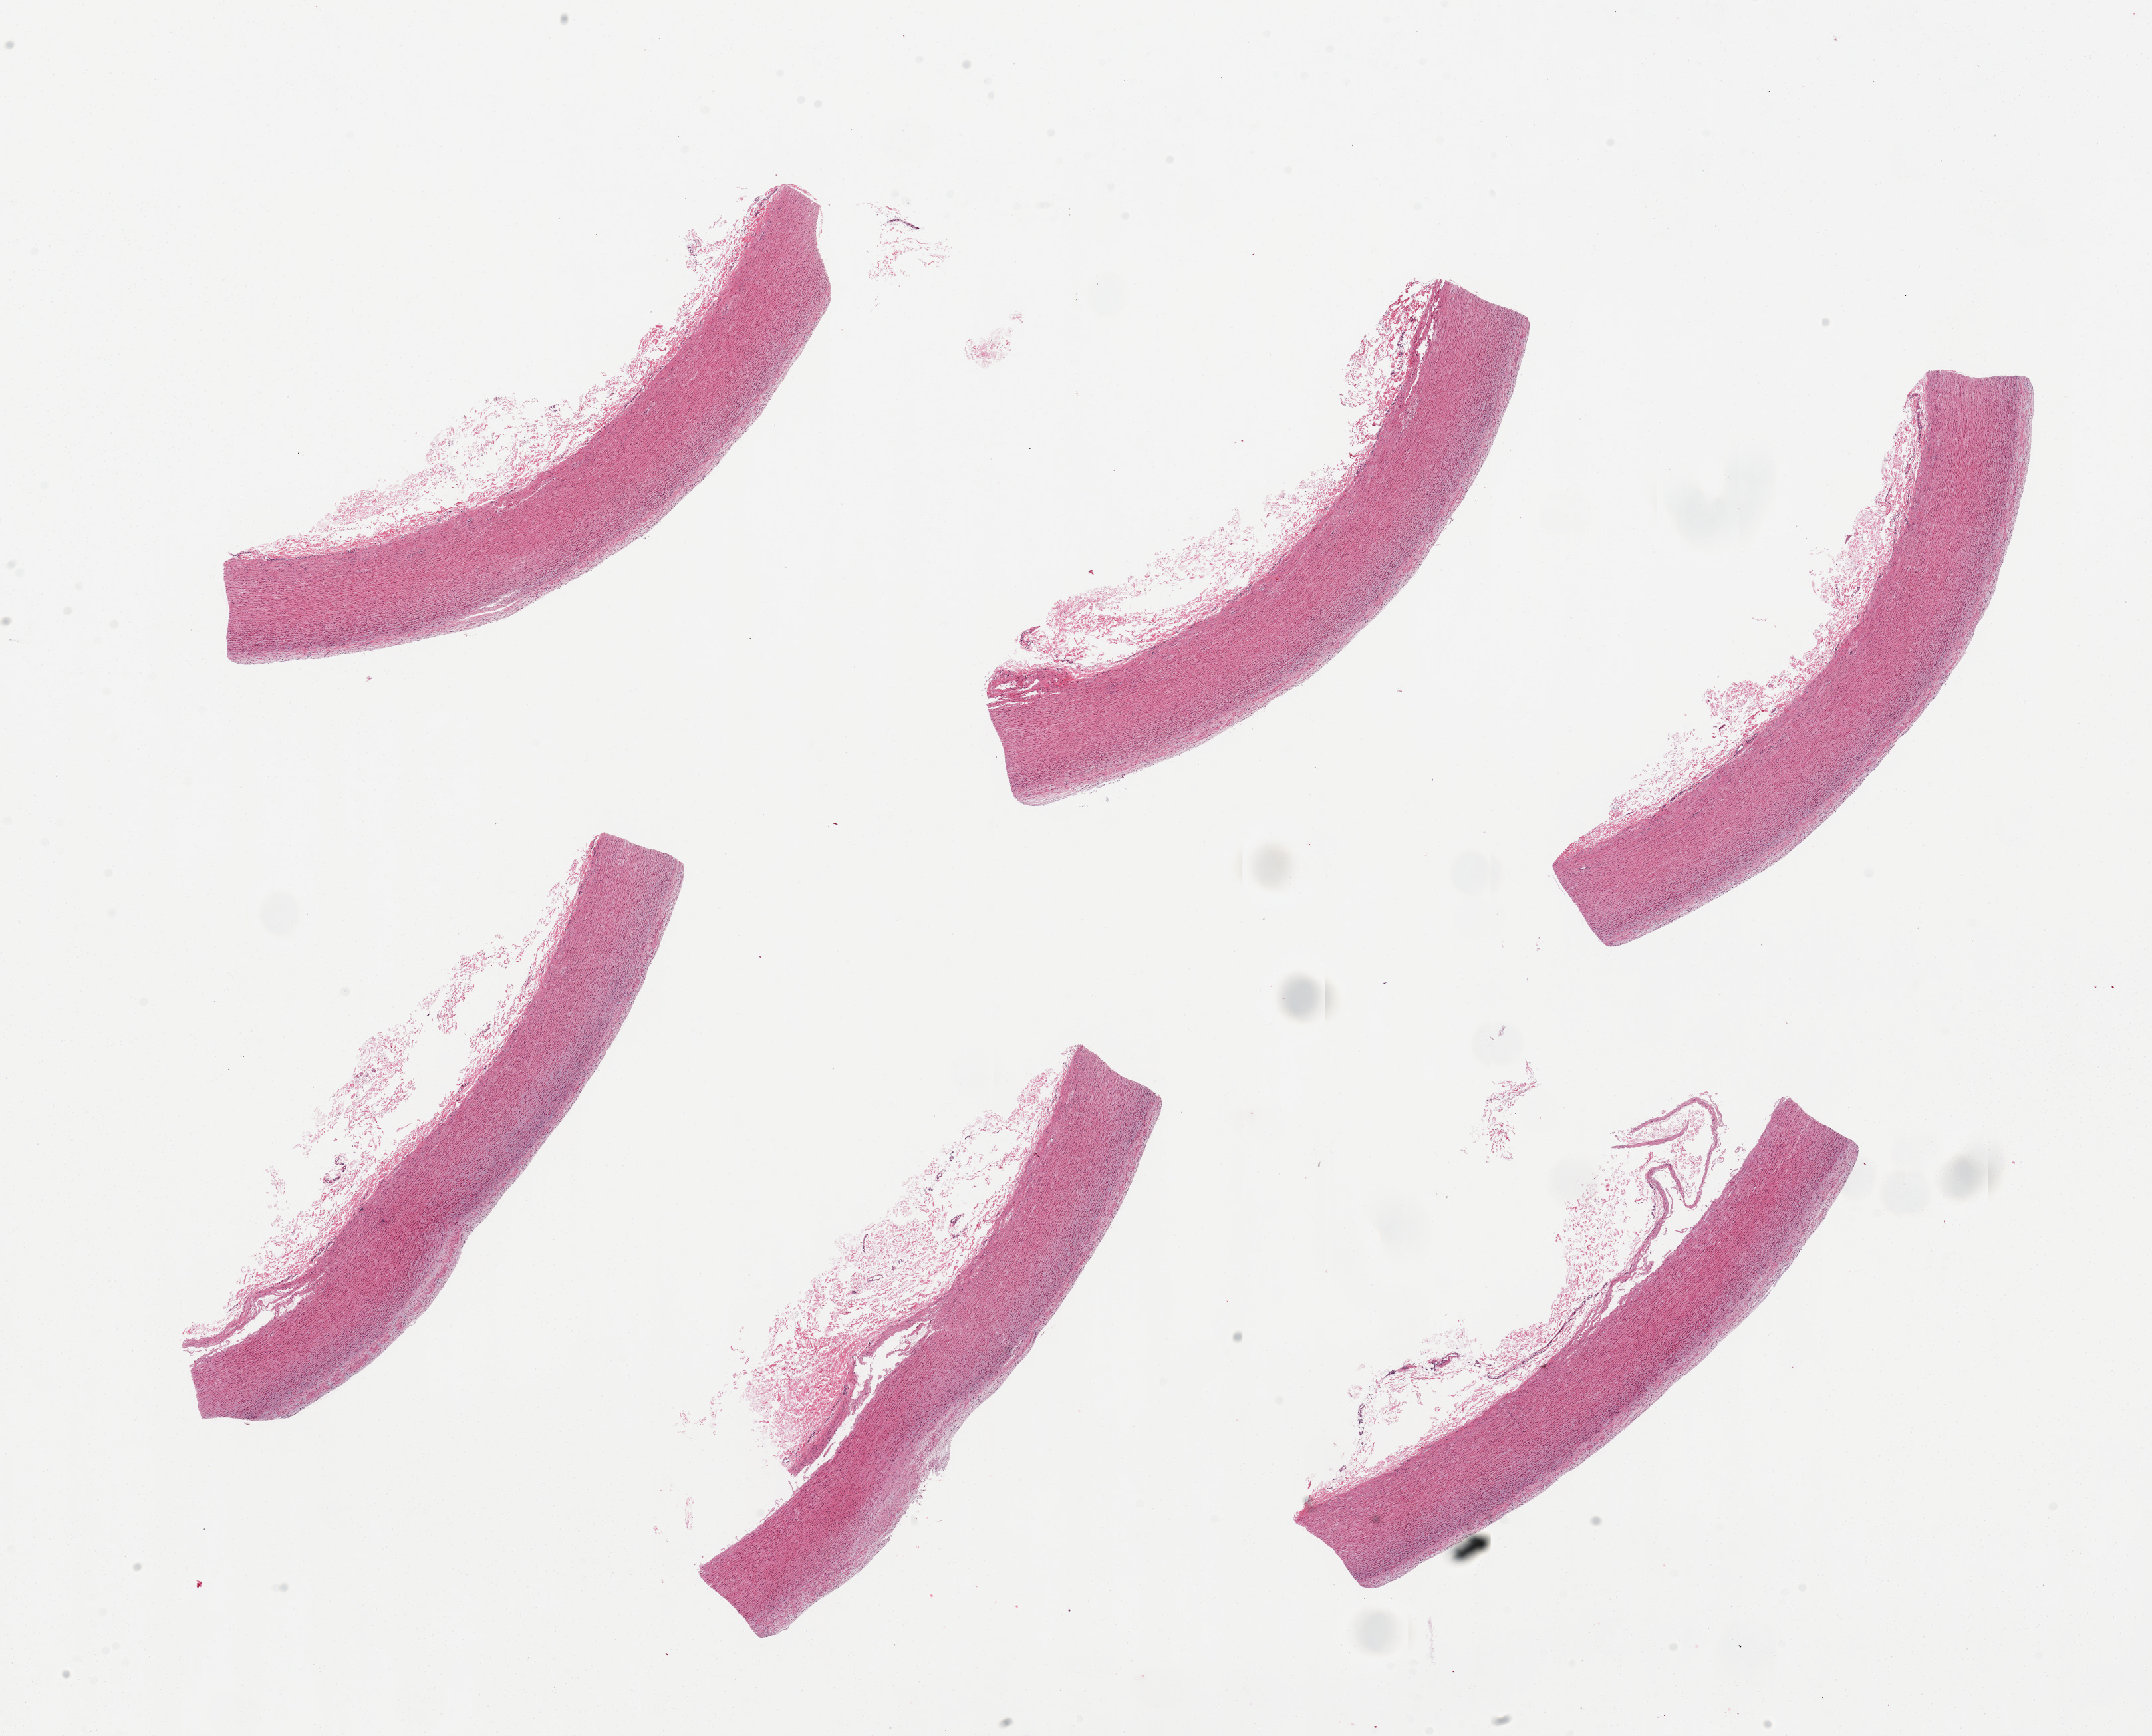
Whole-slide image, haematoxylin and eosin stain, brightfield — a low-resolution overview of the entire scanned area, about 25.6 x 20.6 mm. PAXgene-fixed, paraffin-embedded tissue. Target tissue: aorta. Donor tissue sample.
- reviewer comment on this tissue sample: 6 pieces, up to 8x2mm; adherent fat/serosa up to 1mm on all